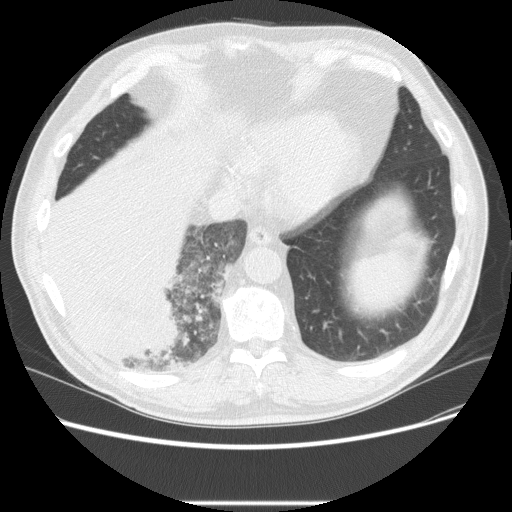
Low-dose screening chest CT, one axial slice; position 58 of 233 along the scan axis; reconstruction kernel STANDARD; lung window (W 1500 / L -600 HU); 2.5 mm slice thickness; 512 × 512 image matrix, field of view 380 × 380 mm.
Annotated regions visible in this slice (manually delineated by an expert):
- lesion 3 (tumor, lower lobe of right lung): bounding box (x1, y1, x2, y2) in pixels: (47, 190, 182, 372)